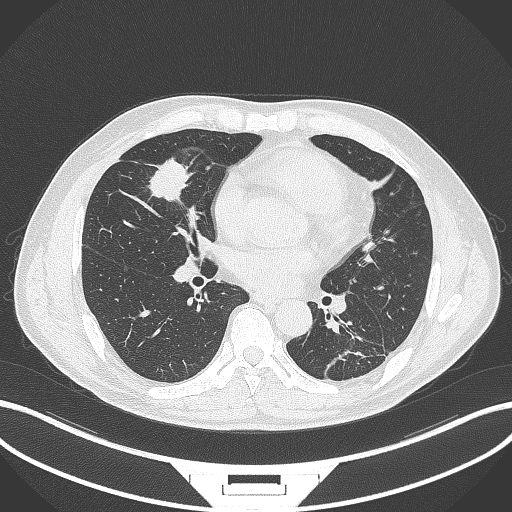
Chest CT, one axial slice; position 139 of 399 along the scan axis; lung window (W 1500 / L -600 HU); 512 × 512 image matrix, field of view 400 × 400 mm. Patient: male, 59 years. Case-level facts recorded for this patient, not image findings: clinical TNM (as recorded): T2a N1 M0.
Outlined on this slice (rectangle marked by the reading radiologist):
- lung tumour (recorded histology: adenocarcinoma): bounding box (x1, y1, x2, y2) in pixels: (148, 155, 197, 208)